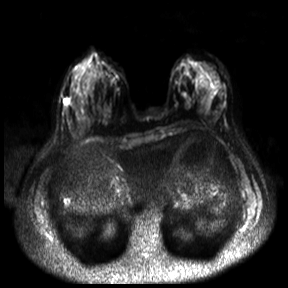
Breast MRI, one axial slice. Position 10 of 30 along the scan axis. Diffusion-weighted series; image 2 of 4 stored at this slice position (different b-values; order by instance number). 3 T. 288 × 288 image matrix. Female patient.
Annotated regions visible in this slice (expert manual segmentation):
- tumour on diffusion-weighted imaging: bounding box (x1, y1, x2, y2) in pixels: (65, 100, 70, 106)